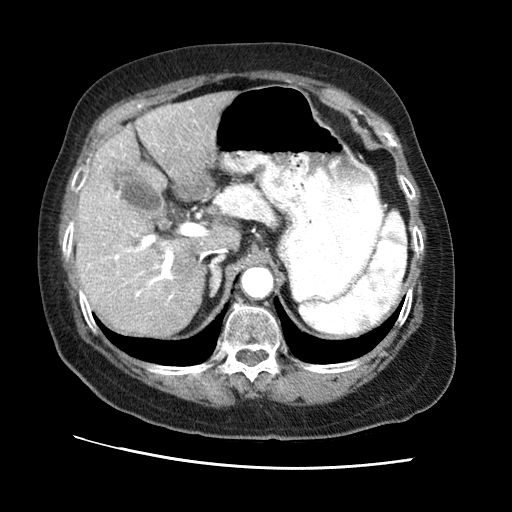
Contrast-enhanced abdominal CT (liver protocol), one axial slice; position 40 of 65 along the scan axis; reconstruction kernel STANDARD; 120 kVp; soft-tissue window (W 400 / L 40 HU); 512 × 512 image matrix, field of view 340 × 340 mm. Case-level facts recorded for this patient, not image findings: diagnosis: hepatocellular carcinoma (patient treated with transarterial chemoembolisation; whether this scan precedes or follows treatment is not stated here); TNM stage (as recorded): Stage-II; Child-Pugh class: A.
Structures marked on this image (semi-automatically segmented with operator editing):
- liver parenchyma outside the tumour (the mass and vessels are separate outlines, so this box may not span the whole liver): bounding box <76,92,240,336> (left, top, right, bottom; pixels)
- liver vessels: <88,108,208,301>